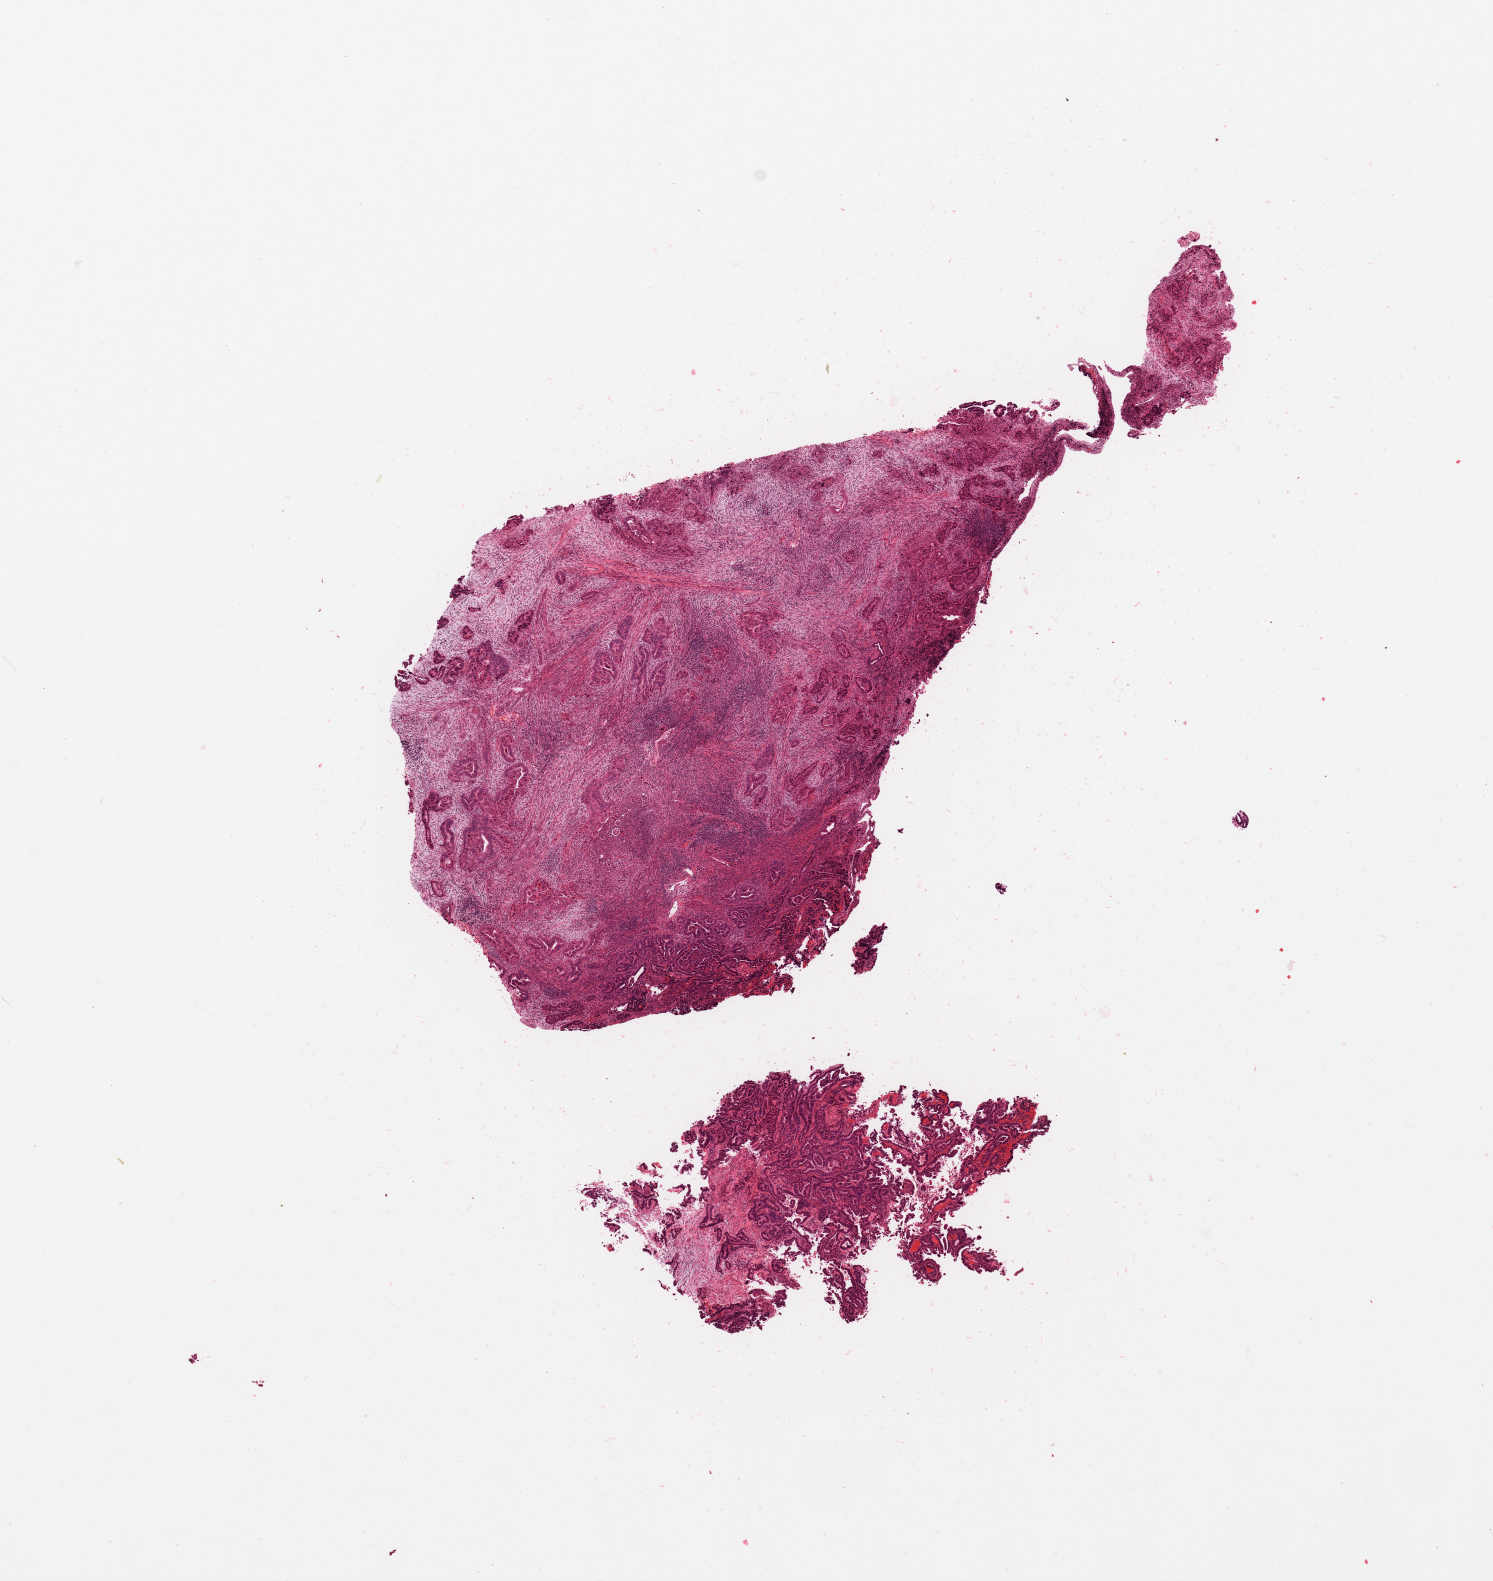
H&E whole-slide image, shown as a low-resolution overview of the whole scanned area (about 11.8 x 12.5 mm, from a 20x scan); uterus, tumour tissue. Female, 73 y/o.
Histologic diagnosis: Endometrioid adenocarcinoma, NOS.